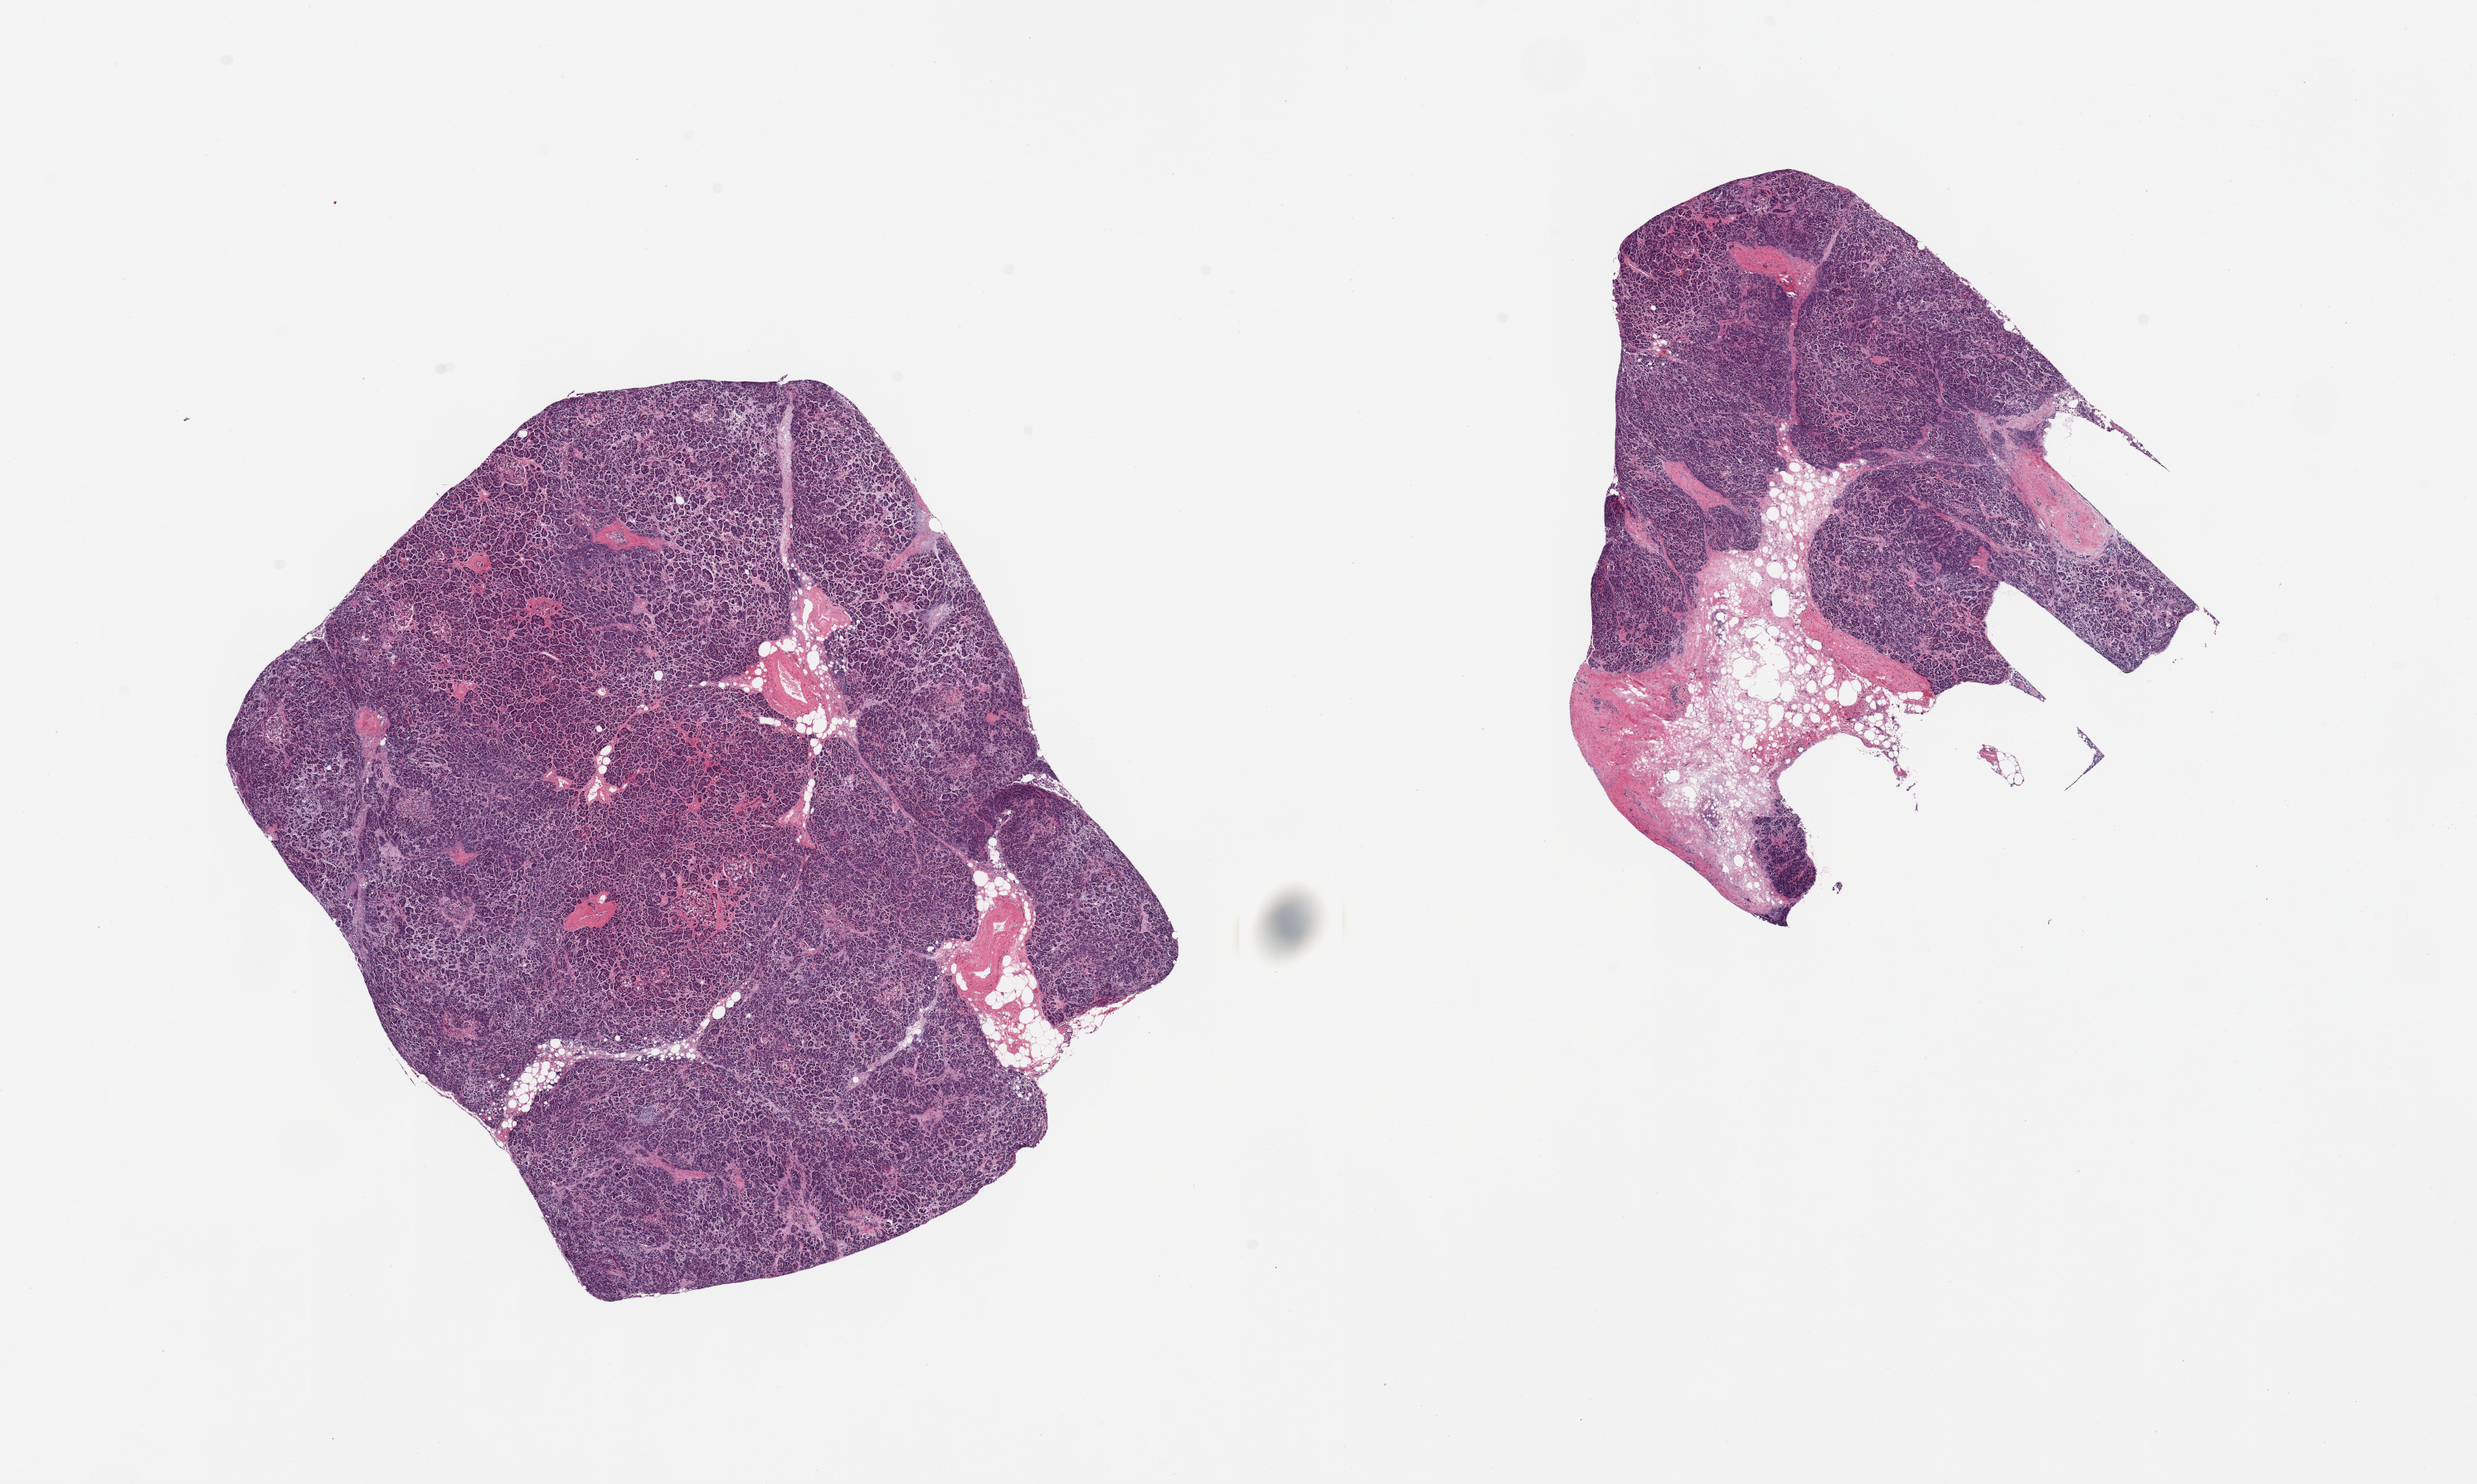
Digitized hematoxylin and eosin (H&E)-stained section — shown as a low-resolution overview of the whole scanned area (about 23.6 x 14.2 mm). PAXgene-fixed paraffin-embedded (PFPE) section. Section of pancreas (target tissue). Donor tissue sample. Male donor.
Pathologist's review note for this sample: 2 pieces; moderate autolysis, some residual islets visualized, interstitial fibrosis, 30% of one piece is fat, fibrous tissue and nerve.